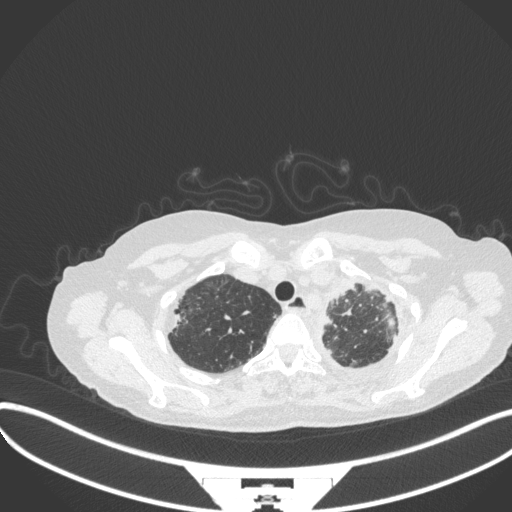
Chest CT, one axial slice. Slice 293 of 373 in the series (ordered by position). Reconstruction kernel B31f. Lung window (W 1500 / L -600 HU). 1 mm slice thickness. 512 × 512 image matrix, field of view 400 × 400 mm. Patient: female, 56 years. Case-level facts recorded for this patient, not image findings: clinical TNM (as recorded): T1 N0 M0.
Structures marked on this image (bounding box drawn by a radiologist):
- lung tumour (recorded histology: adenocarcinoma): bounding box [x1, y1, x2, y2] px = [379, 309, 396, 335]